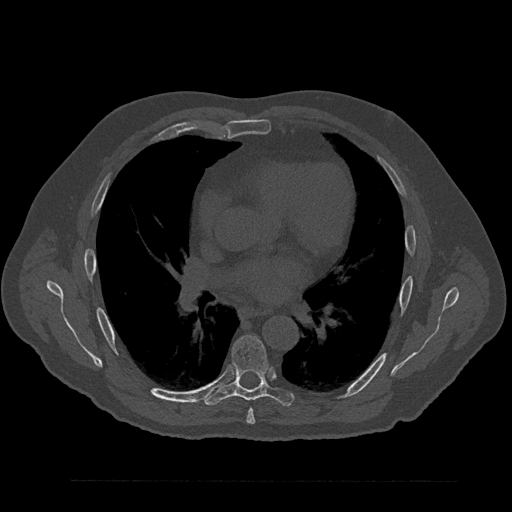
CT including the spine, one axial slice. Slice 516 of 797 in the series (ordered by position). 120 kVp. Bone window (W 1800 / L 400 HU). 0.5 mm slice thickness. 512 × 512 image matrix, field of view 430 × 430 mm. Male patient, age 61 years. Case-level facts recorded for this patient, not image findings: primary cancer: prostate.
Structures marked on this image (semi-automatic segmentation, software-assisted and operator-edited):
- T6 vertebra: box from (x=246, y=409) to (x=256, y=424) px
- T7 vertebra: (x=204, y=335)–(x=294, y=406)